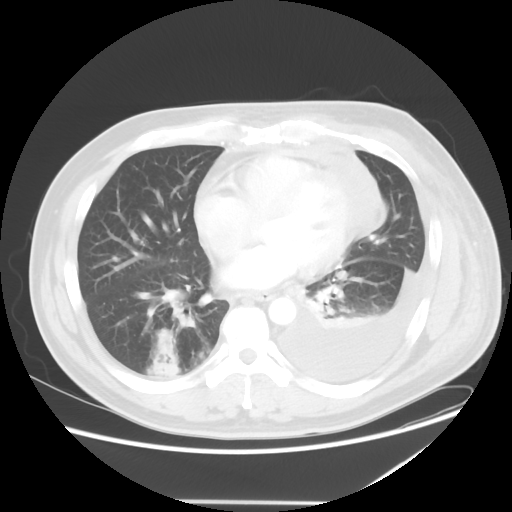
Chest CT, one axial slice; slice 20 of 52 in the series (ordered by position); reconstruction kernel STANDARD; 120 kVp; lung window (W 1500 / L -600 HU); 5 mm slice thickness; 512 × 512 image matrix. Male patient, age 42 years. Case-level facts recorded for this patient, not image findings: clinical TNM (as recorded): T2 N1 M1.
Annotated regions visible in this slice (bounding box drawn by a radiologist):
- lung tumour (recorded histology: adenocarcinoma): bounding box (x1, y1, x2, y2) in pixels: (155, 330, 181, 363)